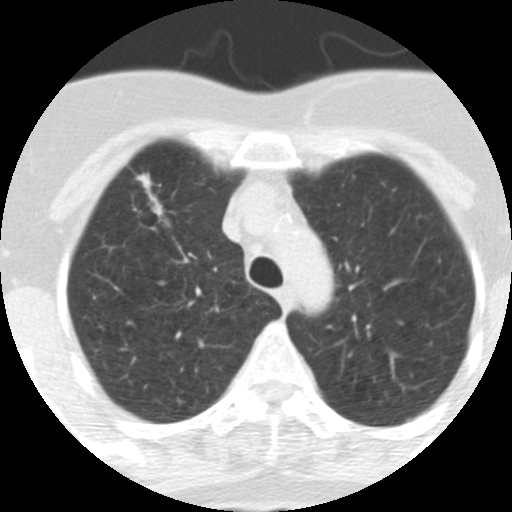
Low-dose screening chest CT, one axial slice. Position 247 of 313 along the scan axis. Reconstruction kernel STANDARD. 120 kVp. Lung window (W 1500 / L -600 HU). 2.5 mm slice thickness. 512 × 512 image matrix.
Structures marked on this image (expert manual segmentation):
- lesion 1 (tumor, upper lobe of right lung): box from (x=136, y=173) to (x=163, y=217) px